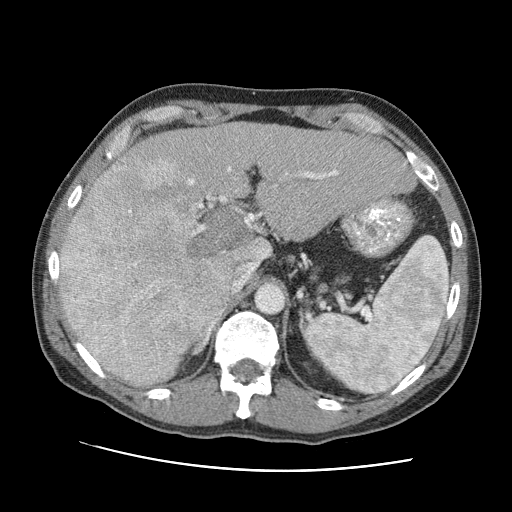
Contrast-enhanced abdominal CT (liver protocol), one axial slice. Slice 56 of 95 in the series (ordered by position). 120 kVp. One of 2 acquisitions stored at this slice position. Soft-tissue window (W 400 / L 40 HU). 512 × 512 image matrix. From the clinical record (not read from this slice): diagnosis: hepatocellular carcinoma (patient treated with transarterial chemoembolisation; whether this scan precedes or follows treatment is not stated here); TNM stage (as recorded): Stage-IVA; Child-Pugh class: A; tumour differentiation: moderately differentiated; tumour nodularity: multinodular.
Structures marked on this image (semi-automatically segmented with operator editing):
- liver parenchyma outside the tumour (the mass and vessels are separate outlines, so this box may not span the whole liver): box from (x=60, y=122) to (x=416, y=386) px
- mass: (x=59, y=156)–(x=256, y=385)
- liver vessels: (x=61, y=167)–(x=338, y=321)